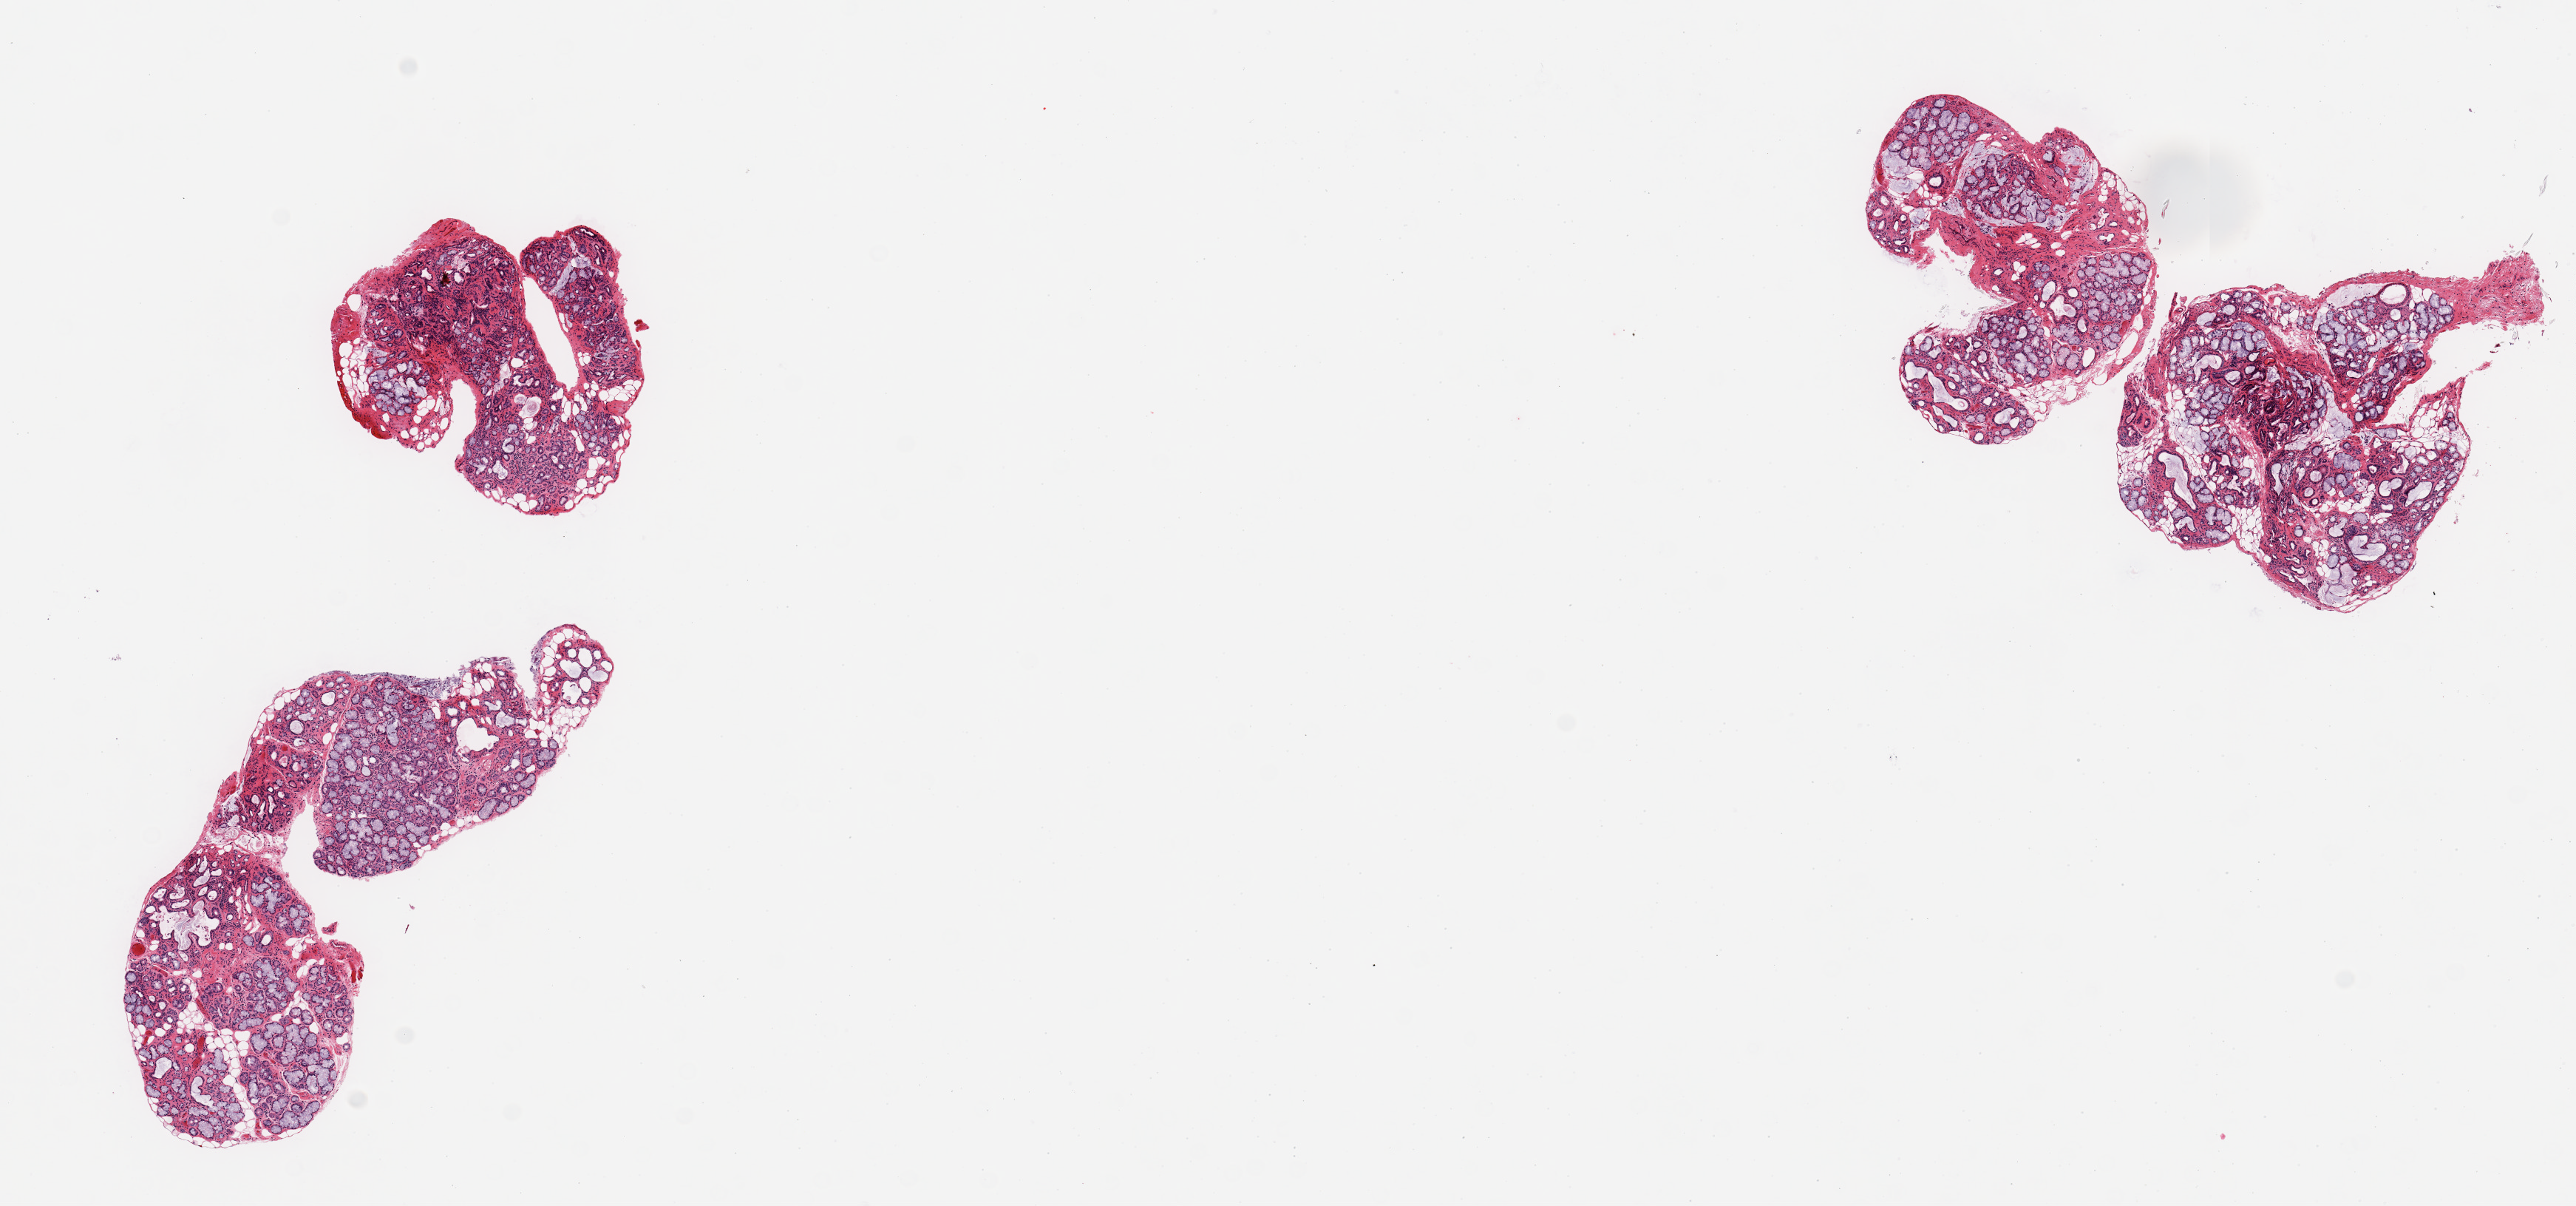
Hematoxylin and eosin (H&E) whole-slide image, brightfield — shown as a low-resolution overview of the whole scanned area (about 13.8 x 6.4 mm), PAXgene-fixed paraffin-embedded (PFPE) section, target tissue: minor salivary gland, tissue donor sample. Male donor.
Reviewer comment on this tissue sample: 4 pieces; well dissected; focal interstitial scarring and atrophy; 20% fat content.